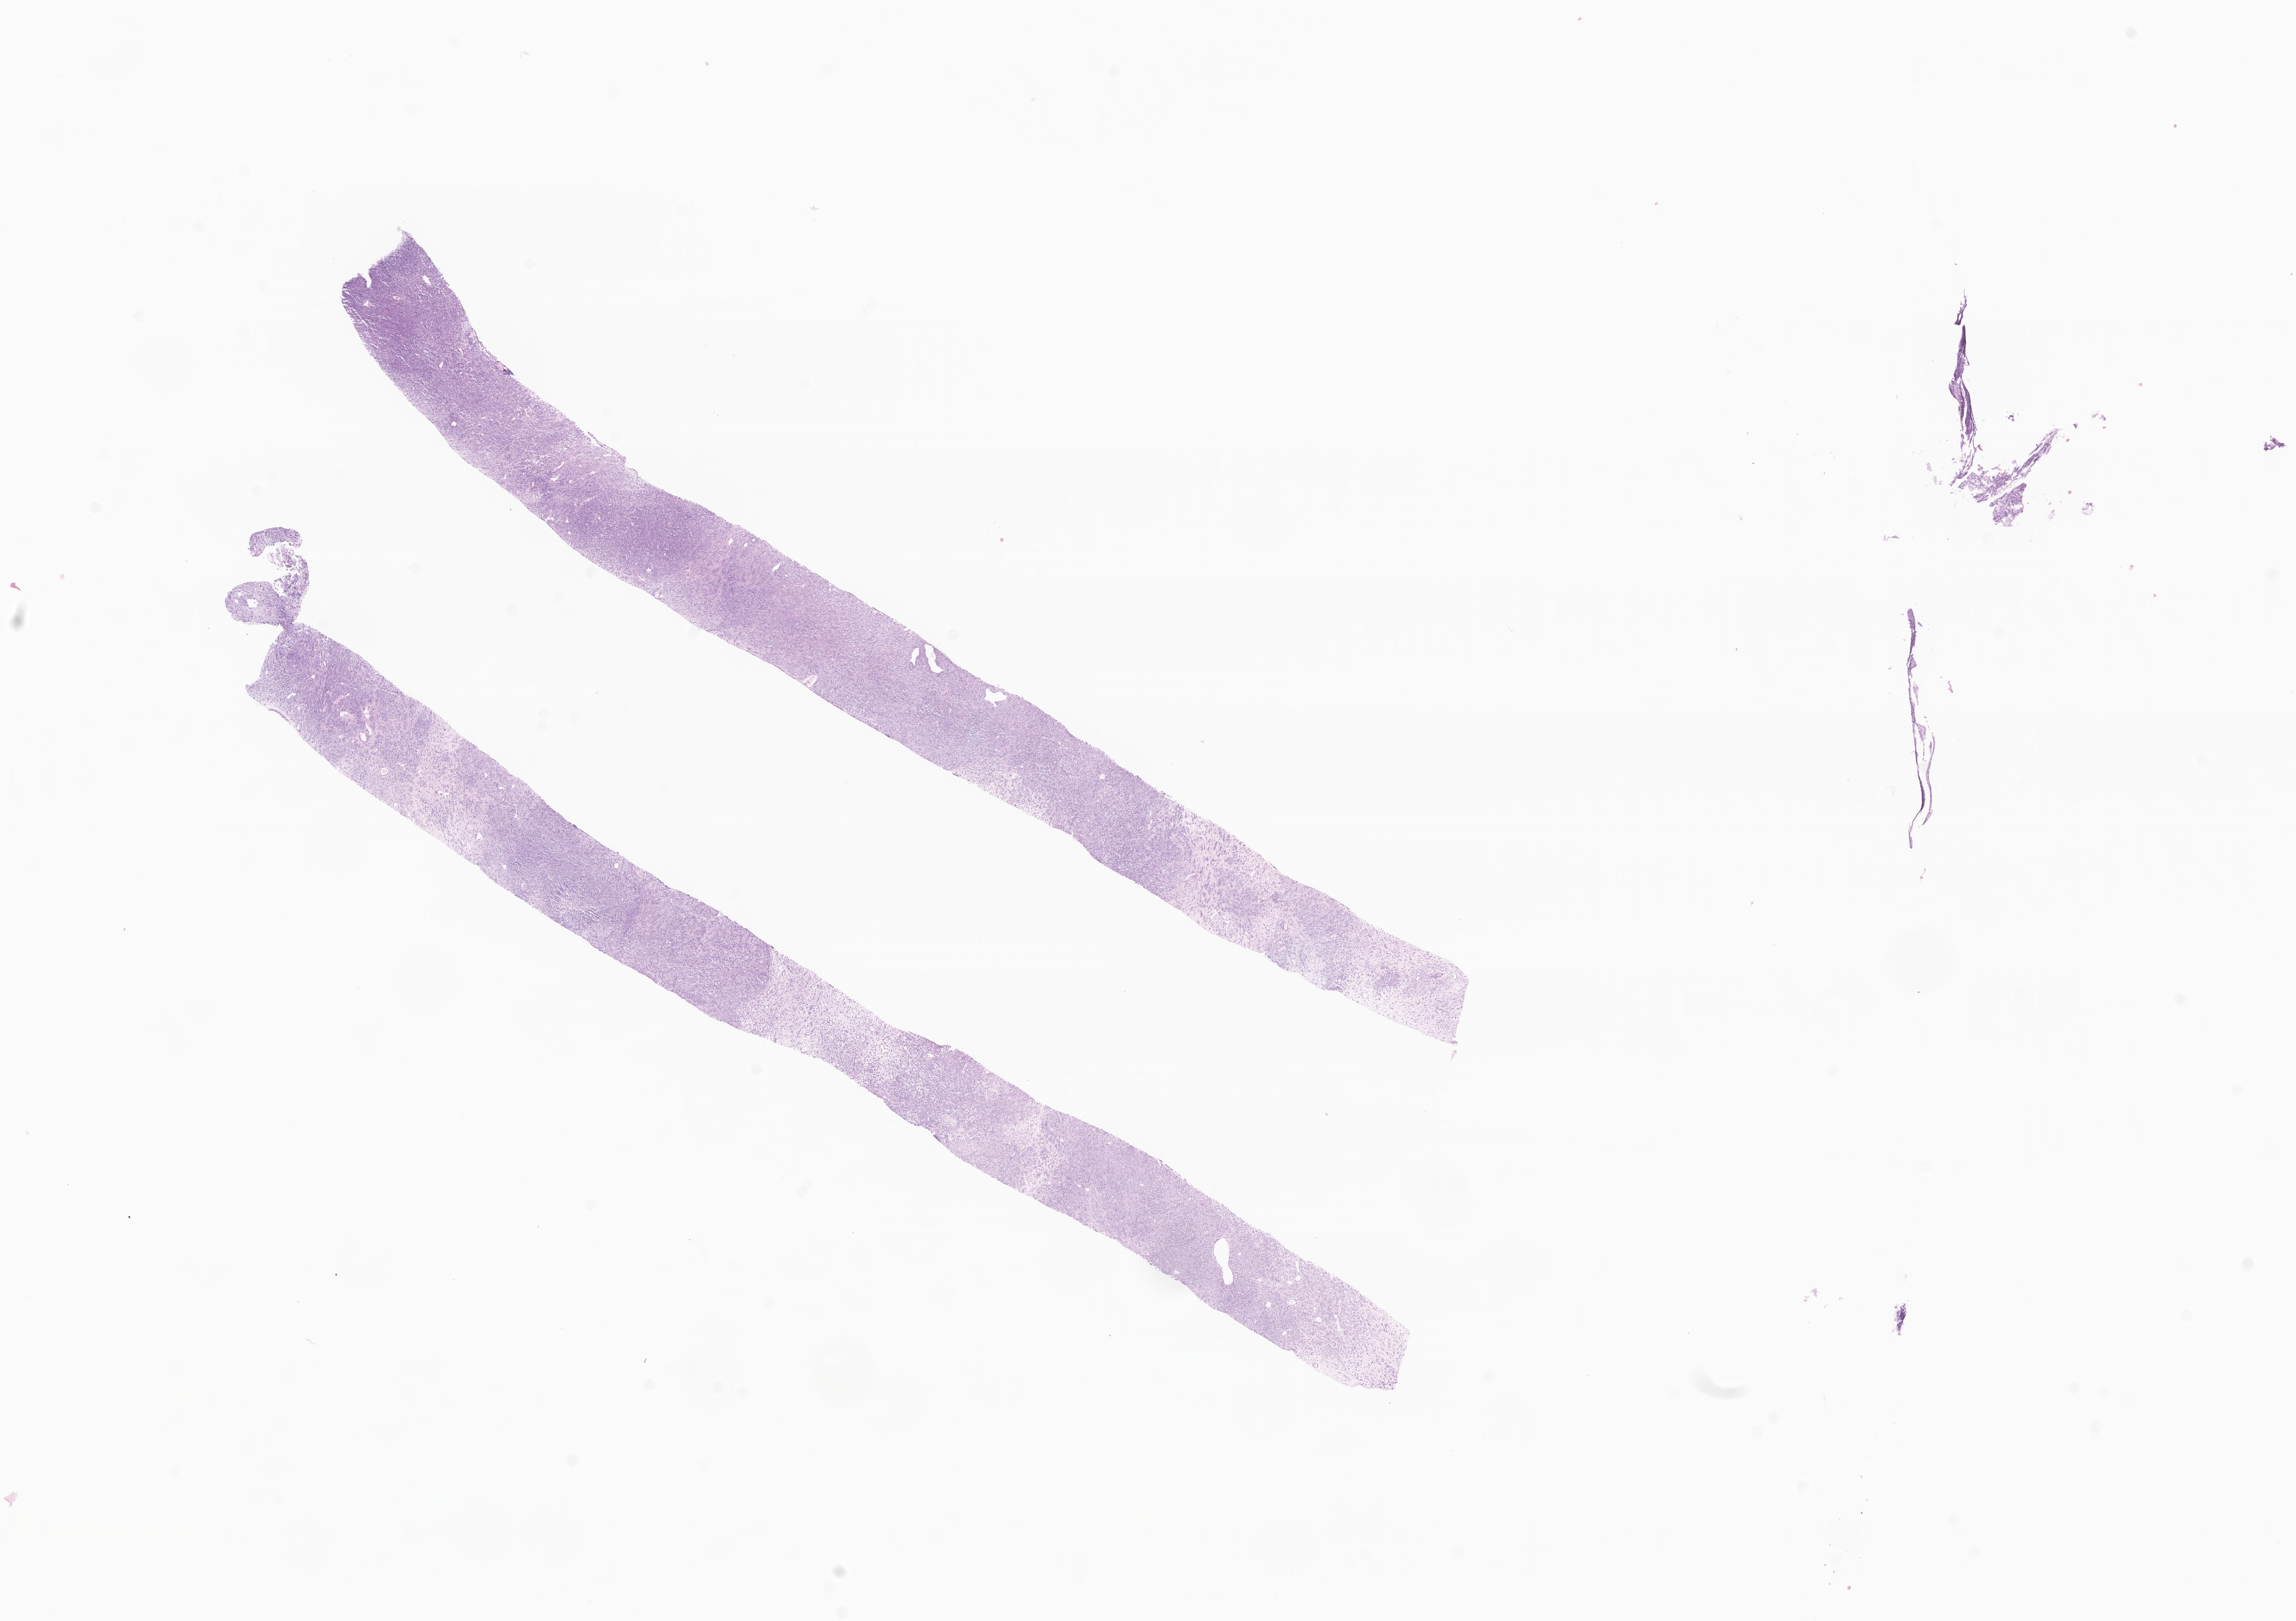
Whole-slide image, haematoxylin and eosin stain of tumor tissue from the kidney — low-resolution overview of the scanned area, about 18.8 x 13.3 mm, formalin-fixed, paraffin-embedded (FFPE) tissue. Female patient, age 158 days.
Recorded diagnosis: Rhabdoid tumor, NOS.